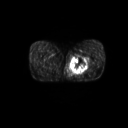
FDG PET of an extremity soft-tissue mass (from a PET/CT study), one axial slice; slice 23 of 267 in the series (ordered by position); 128 × 128 image matrix, field of view 600 × 600 mm. Patient: male, 59 years. From the clinical record (not read from this slice): histological type: pleiomorphic liposarcoma; grade: high; site of the primary tumour: left thigh.
Structures marked on this image (expert contour drawn on MRI and transferred to this co-registered scan by the dataset authors):
- gross tumour volume including surrounding oedema: box from (x=70, y=55) to (x=91, y=75) px
- gross tumour volume (mass): (x=71, y=56)–(x=88, y=74)